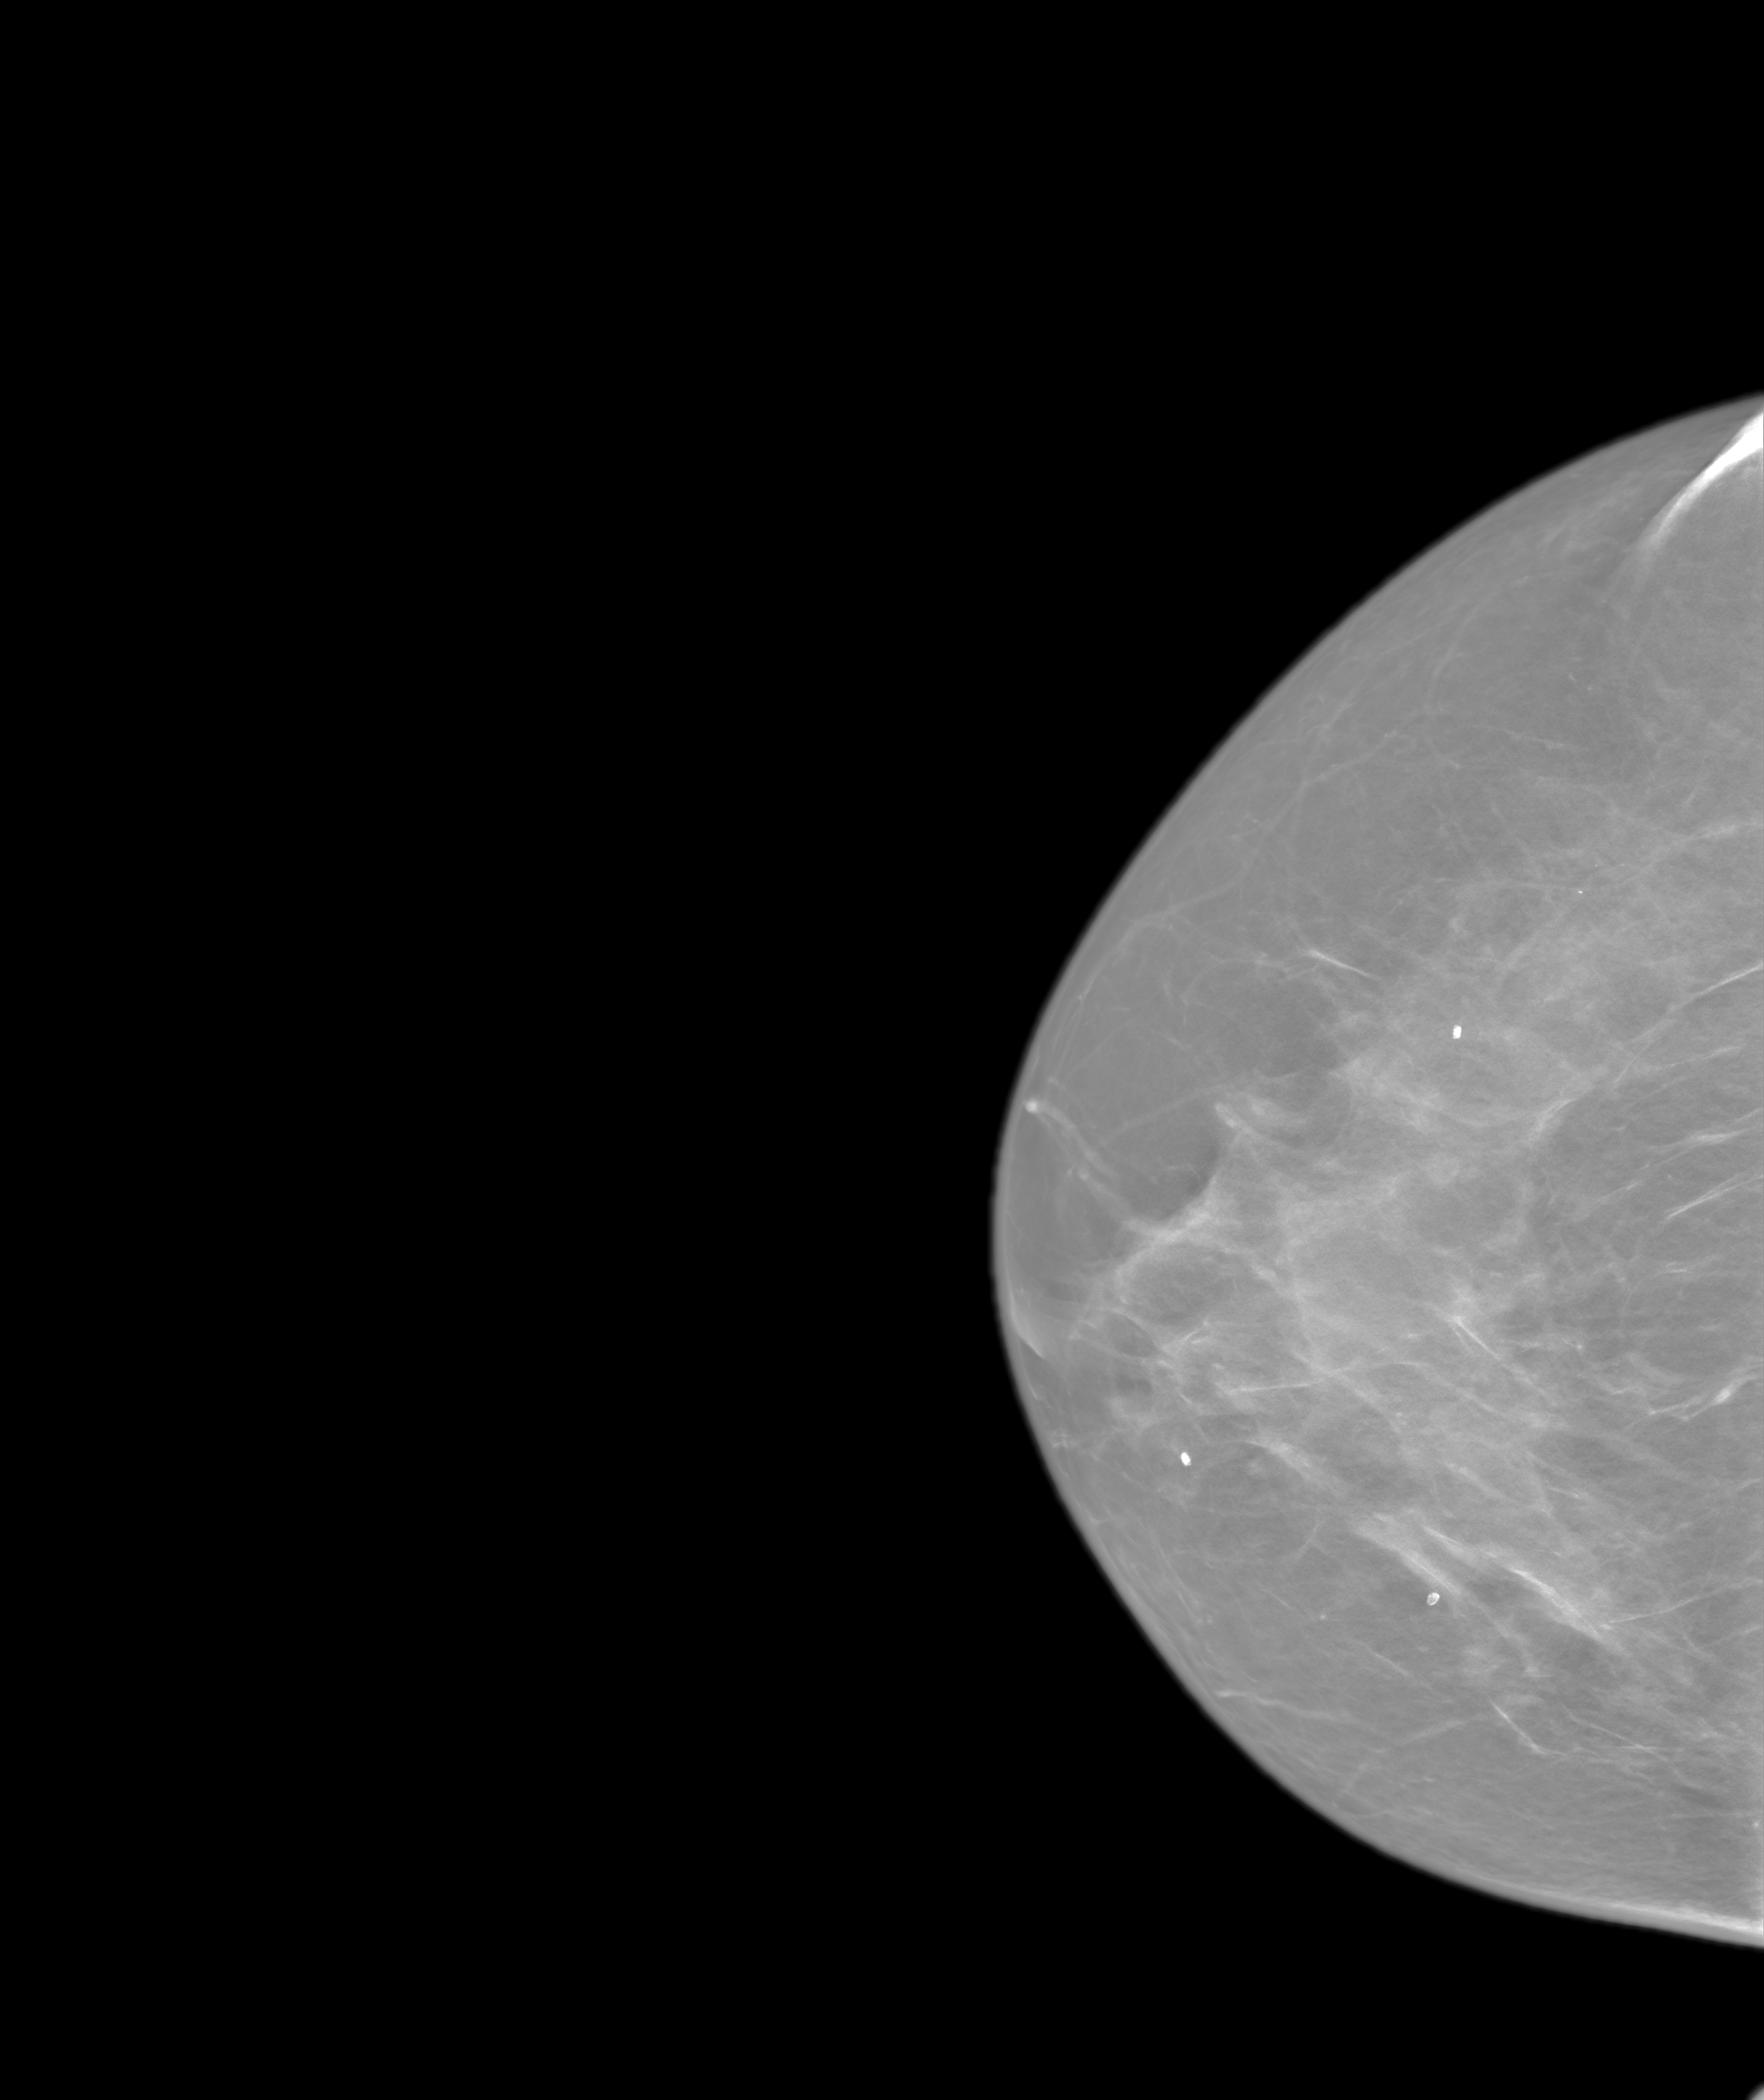
Screening examination. Patient aged 48 years (female).
Image type: synthesized 2-D view from tomosynthesis. Breast: right. Projection: cranio-caudal projection.